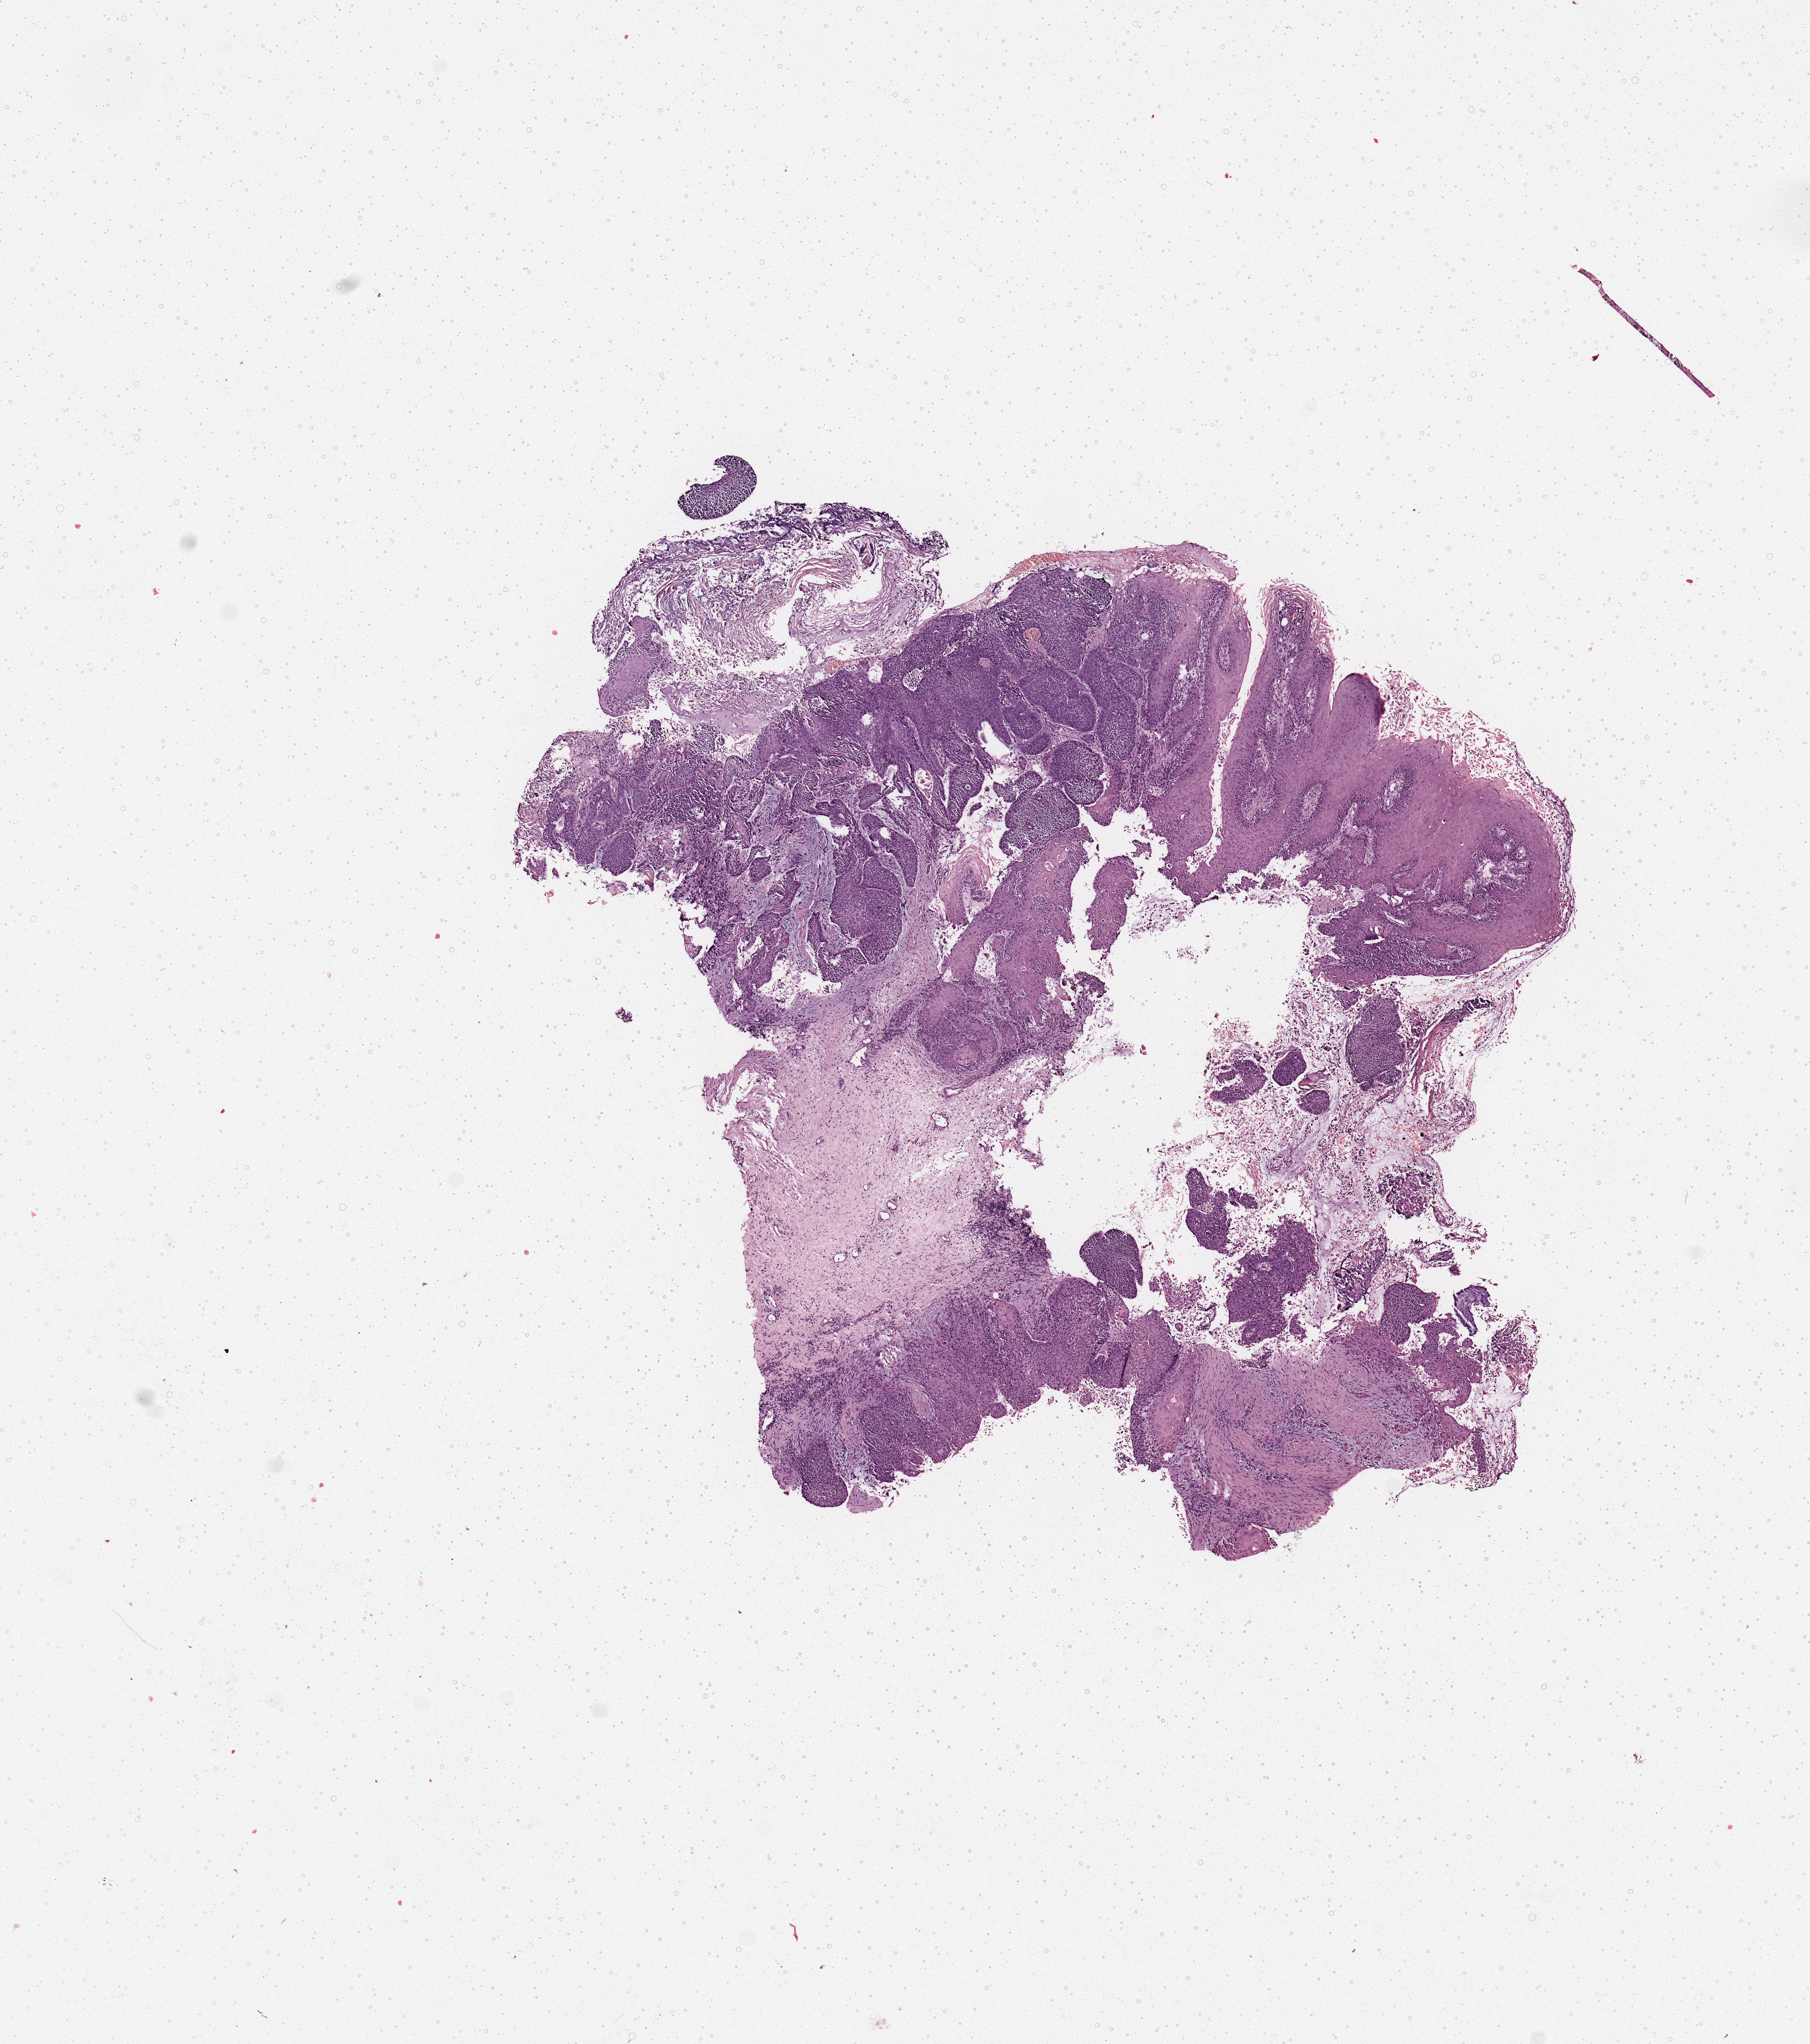
Hematoxylin and eosin (H&E) stained whole-slide image — low-resolution overview of the scanned area, about 10.8 x 12.2 mm (slide scanned at 20x), head and neck, tissue type not recorded. Patient: male, age 58 years.
Patient diagnosis: Squamous cell carcinoma, NOS (larynx, NOS).